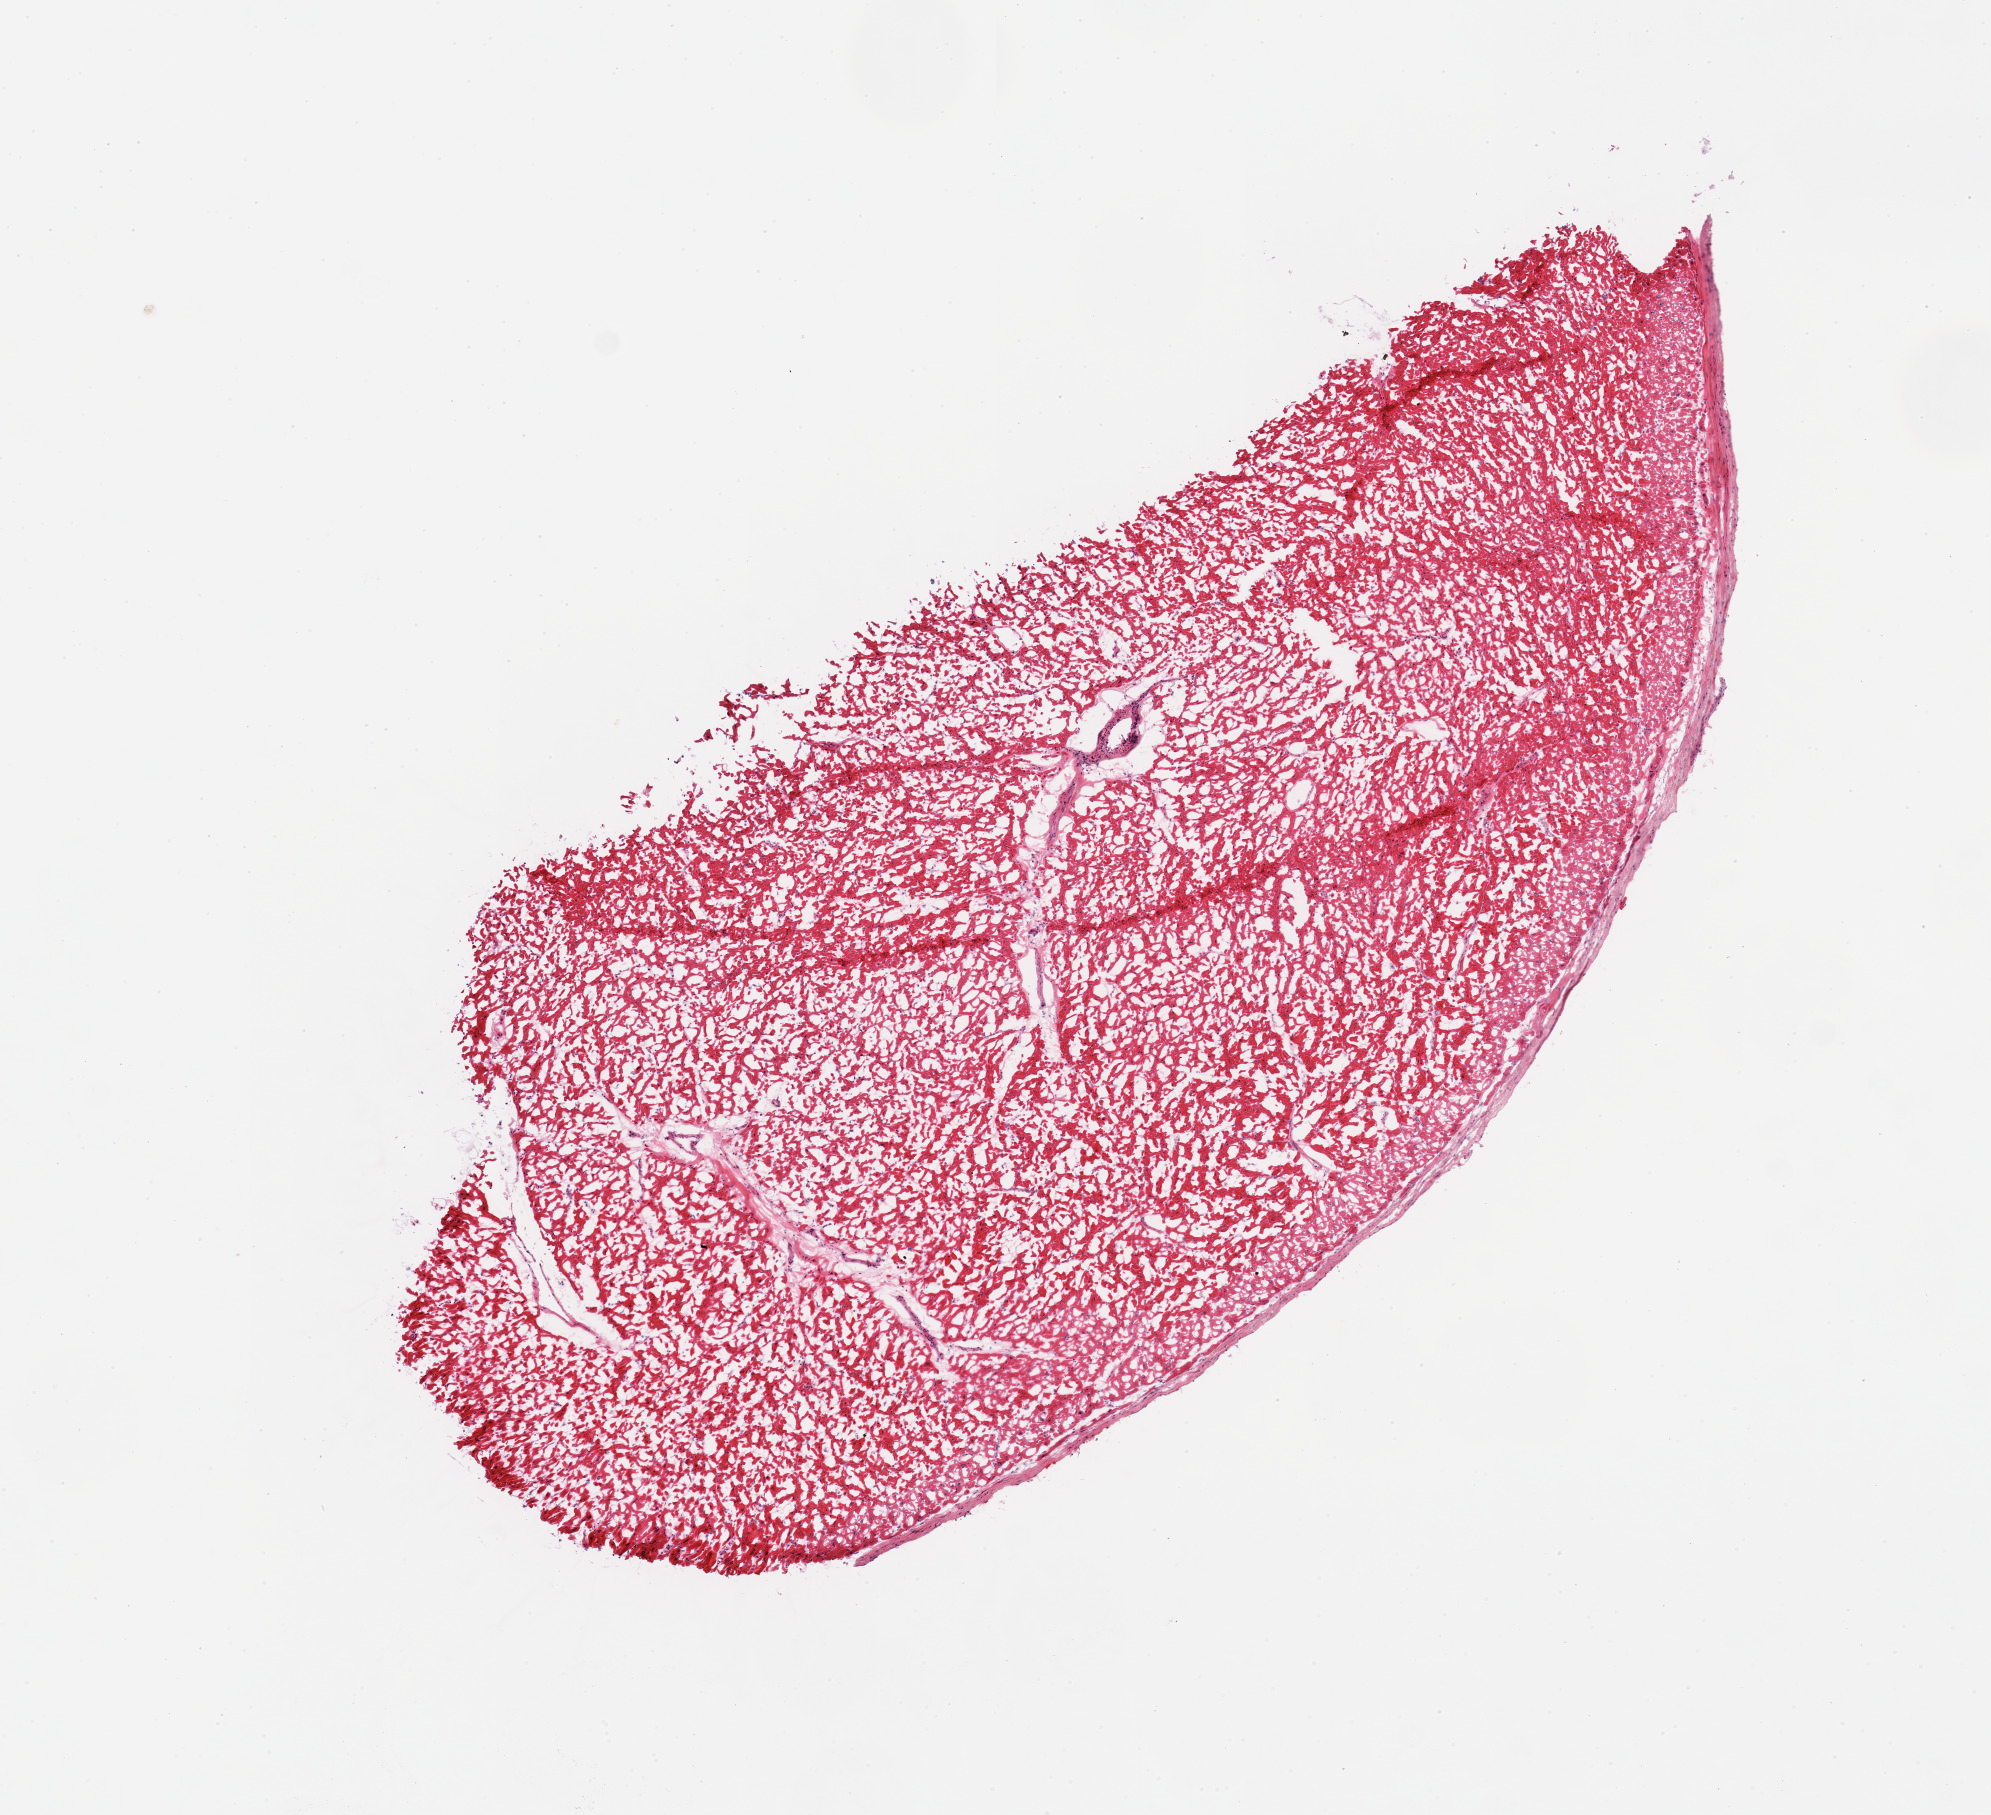
Haematoxylin and eosin whole-slide image — low-resolution overview of the scanned area, about 7.9 x 7.2 mm.
Specimen: frozen section (dry ice); target tissue: heart; tissue donor sample.